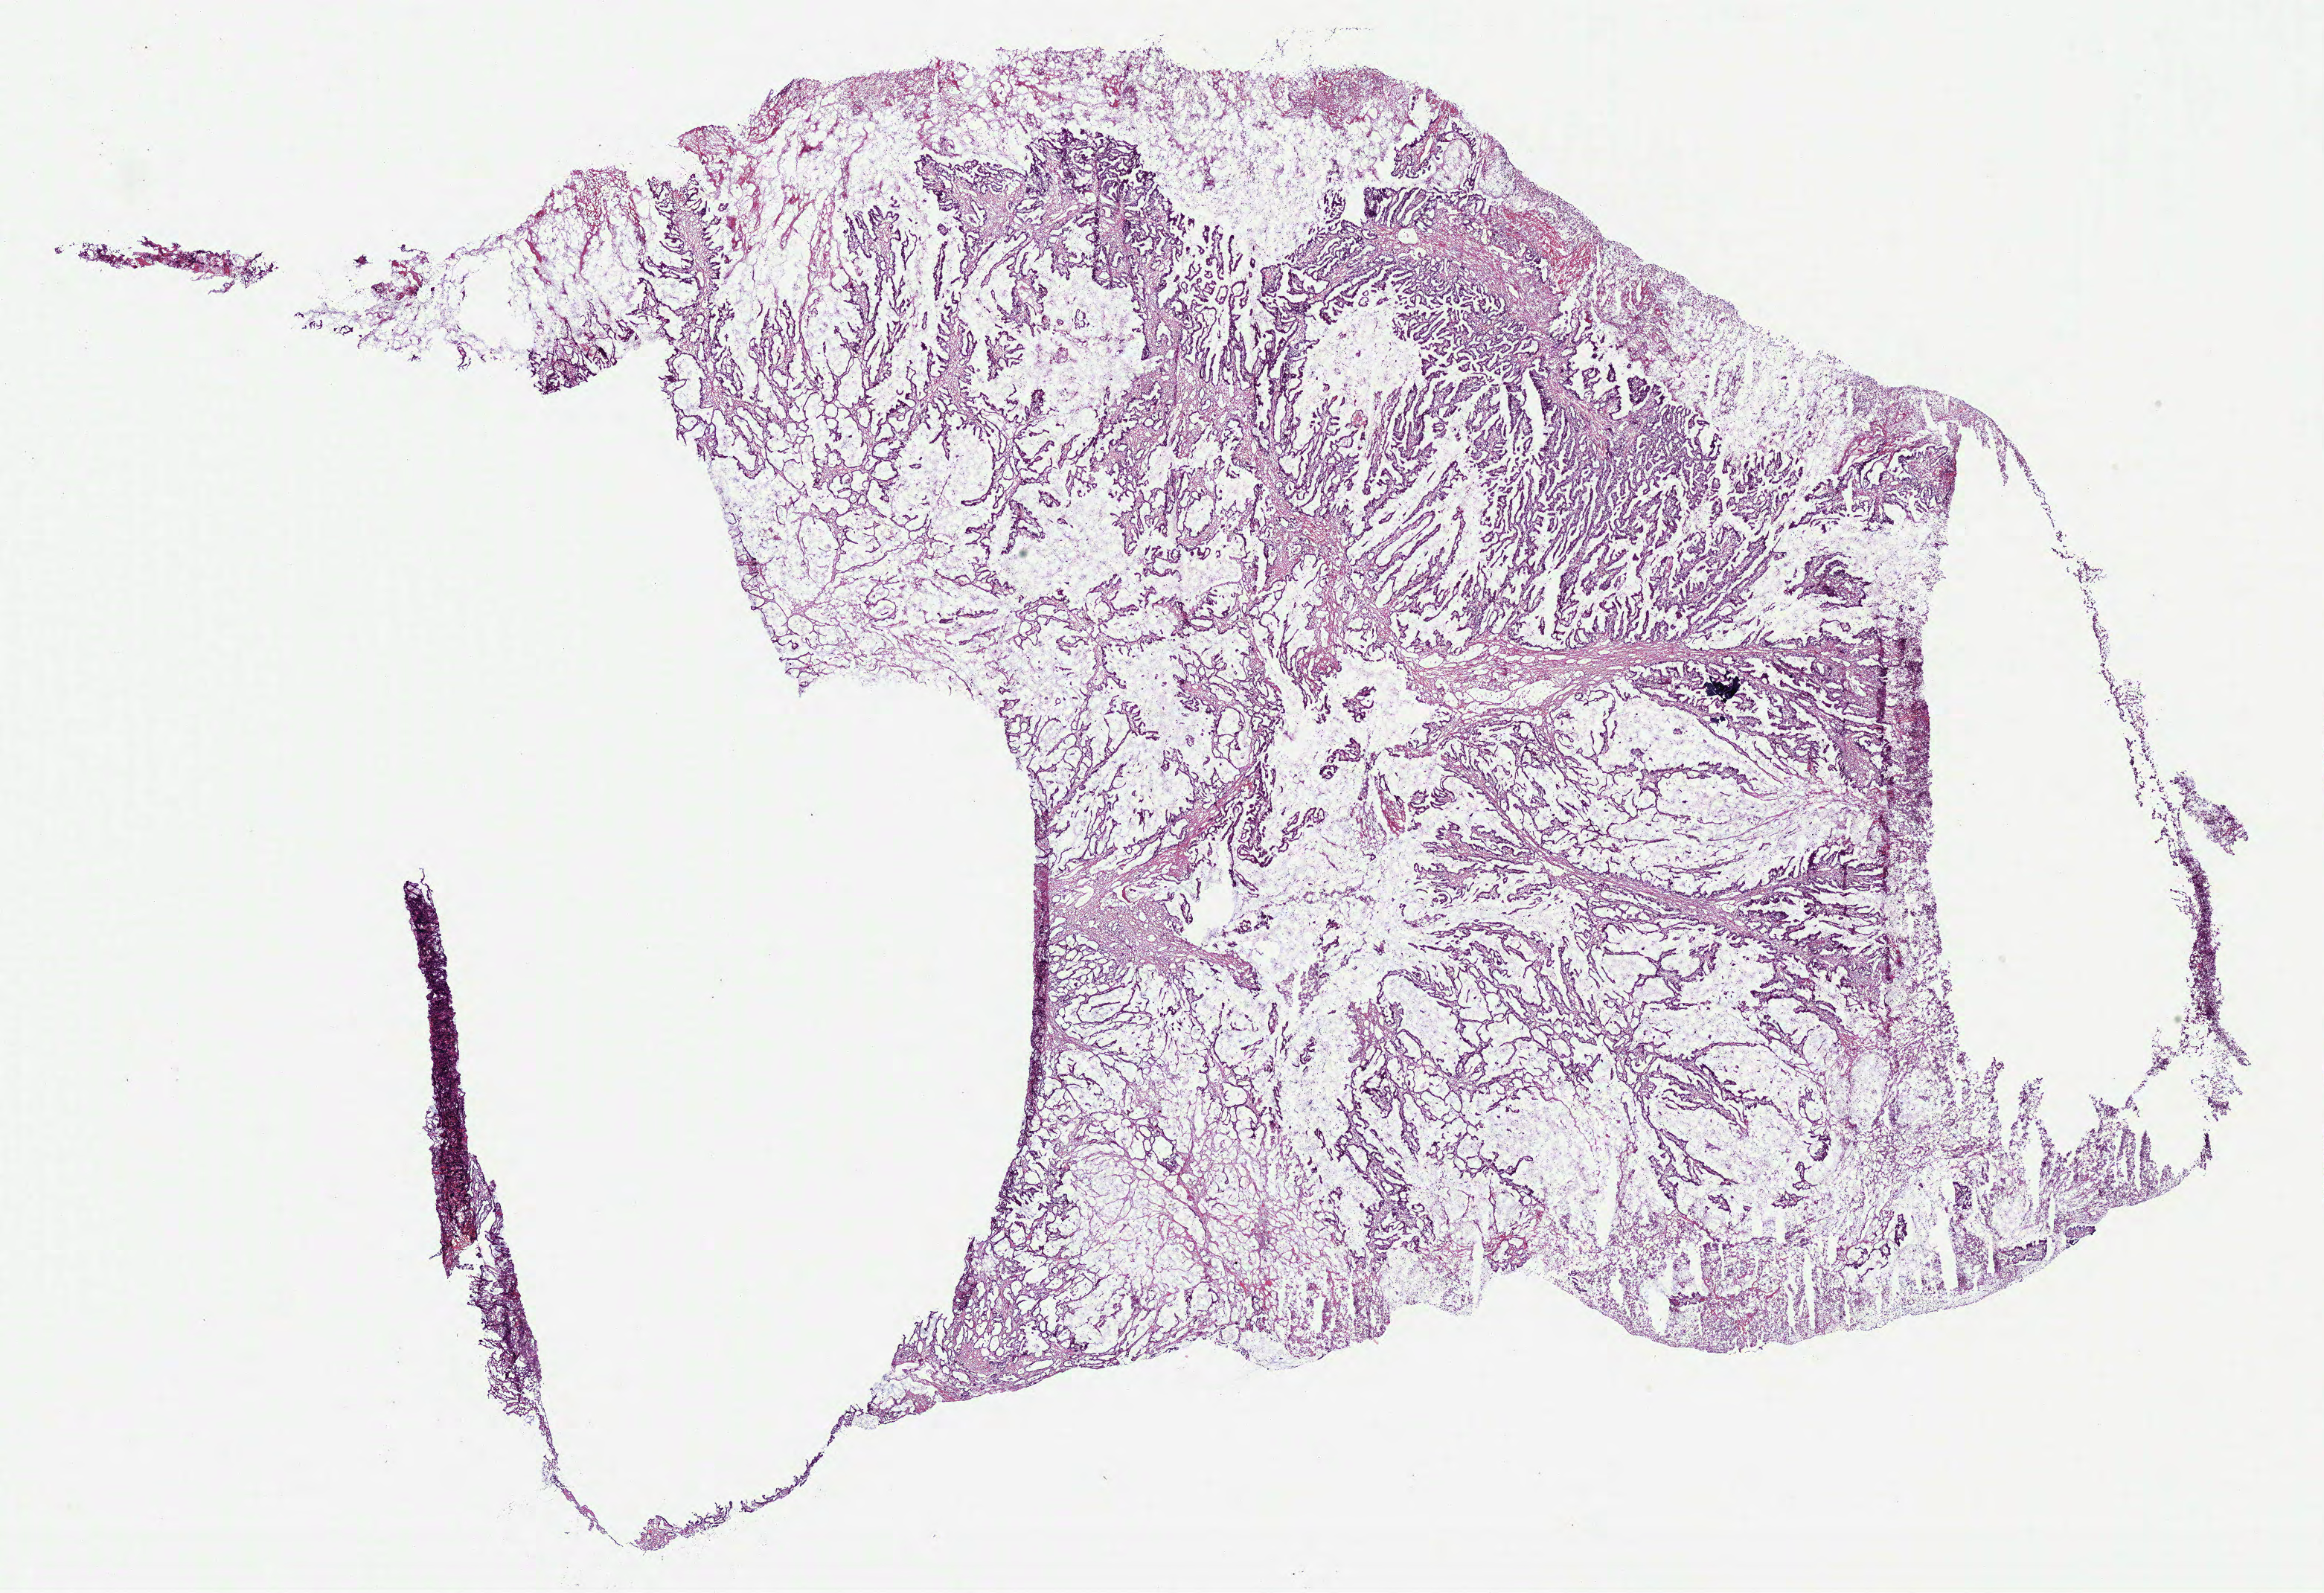
Digitized H&E-stained tissue section (whole slide), a low-resolution overview of the entire scanned area, about 24.6 x 16.9 mm (slide scanned at 40x). Frozen section from the bottom of the tissue portion. Sample: primary tumour, colon. Patient: female, age at initial diagnosis 63 years. Slide review estimates, as recorded: tumour cells 88%, tumour nuclei 75%, normal cells 0%, stromal cells 0%, necrosis 12%. Inflammatory infiltration, as recorded: lymphocyte infiltration 5%, monocyte infiltration 1%, neutrophil infiltration 15%.
* AJCC pathologic stage: IIA (7th edition)
* pathologic diagnosis: Adenocarcinoma, NOS (cecum)
* TNM: T3 N0 M0
* lymph nodes positive (case pathology): 0 of 28 examined